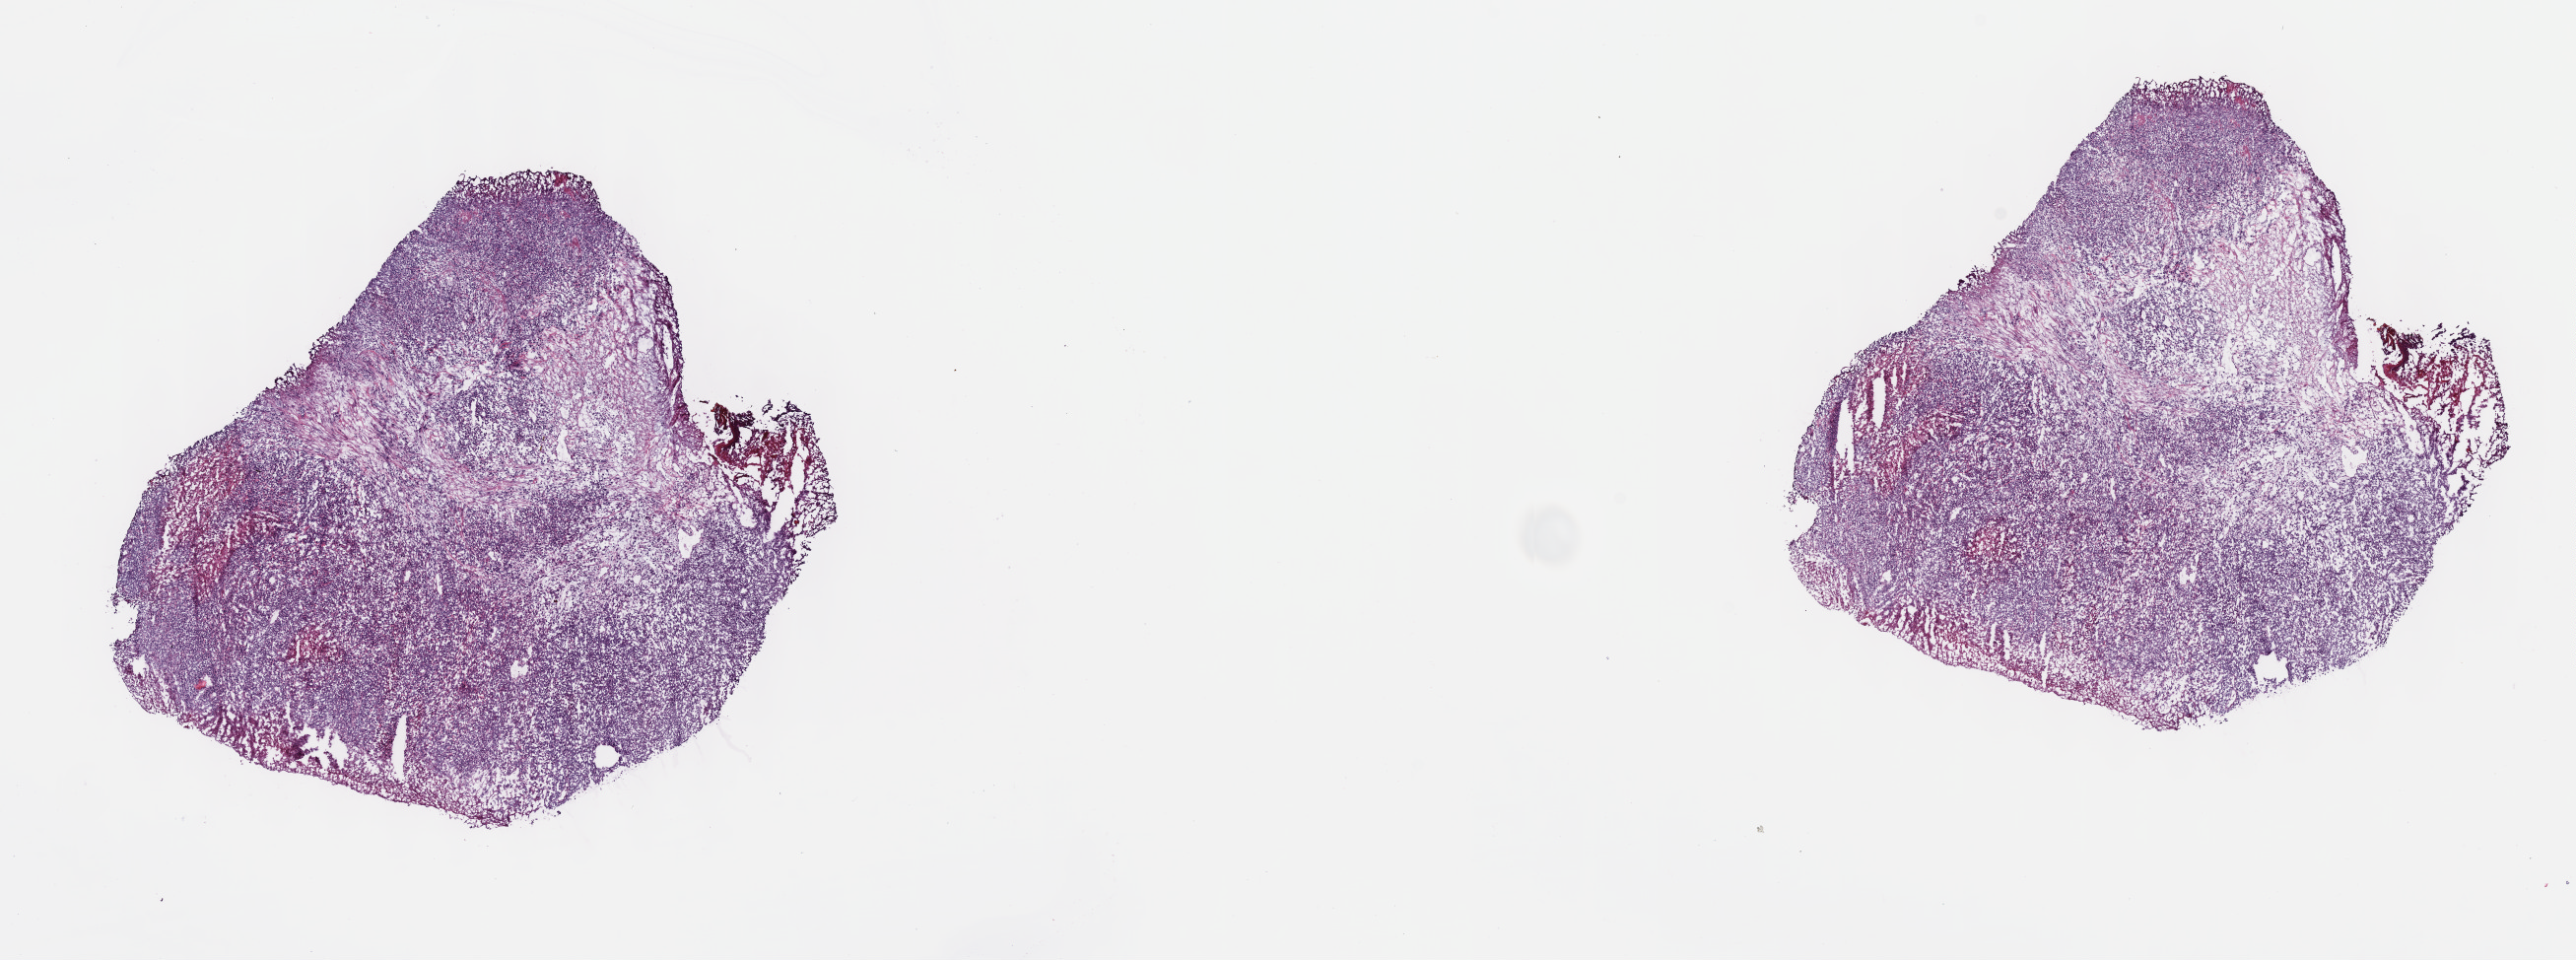
Digitized H&E-stained tissue section (whole slide), a low-resolution overview of the entire scanned area, about 21.1 x 7.9 mm (acquisition: 40x scan), frozen section, bladder, primary tumour sample. Patient: male, age at initial diagnosis 49 years. Histologic grade: high grade. Pathologist review of this section (percent, as recorded): tumour cells 92%, tumour nuclei 75%, normal cells 0%, stromal cells 0%, necrosis 8%. Inflammatory infiltration, as recorded: lymphocyte infiltration 3%, monocyte infiltration 0%, neutrophil infiltration 0%.
AJCC pathologic stage: III. Pathologic diagnosis: Transitional cell carcinoma (lateral wall of bladder).